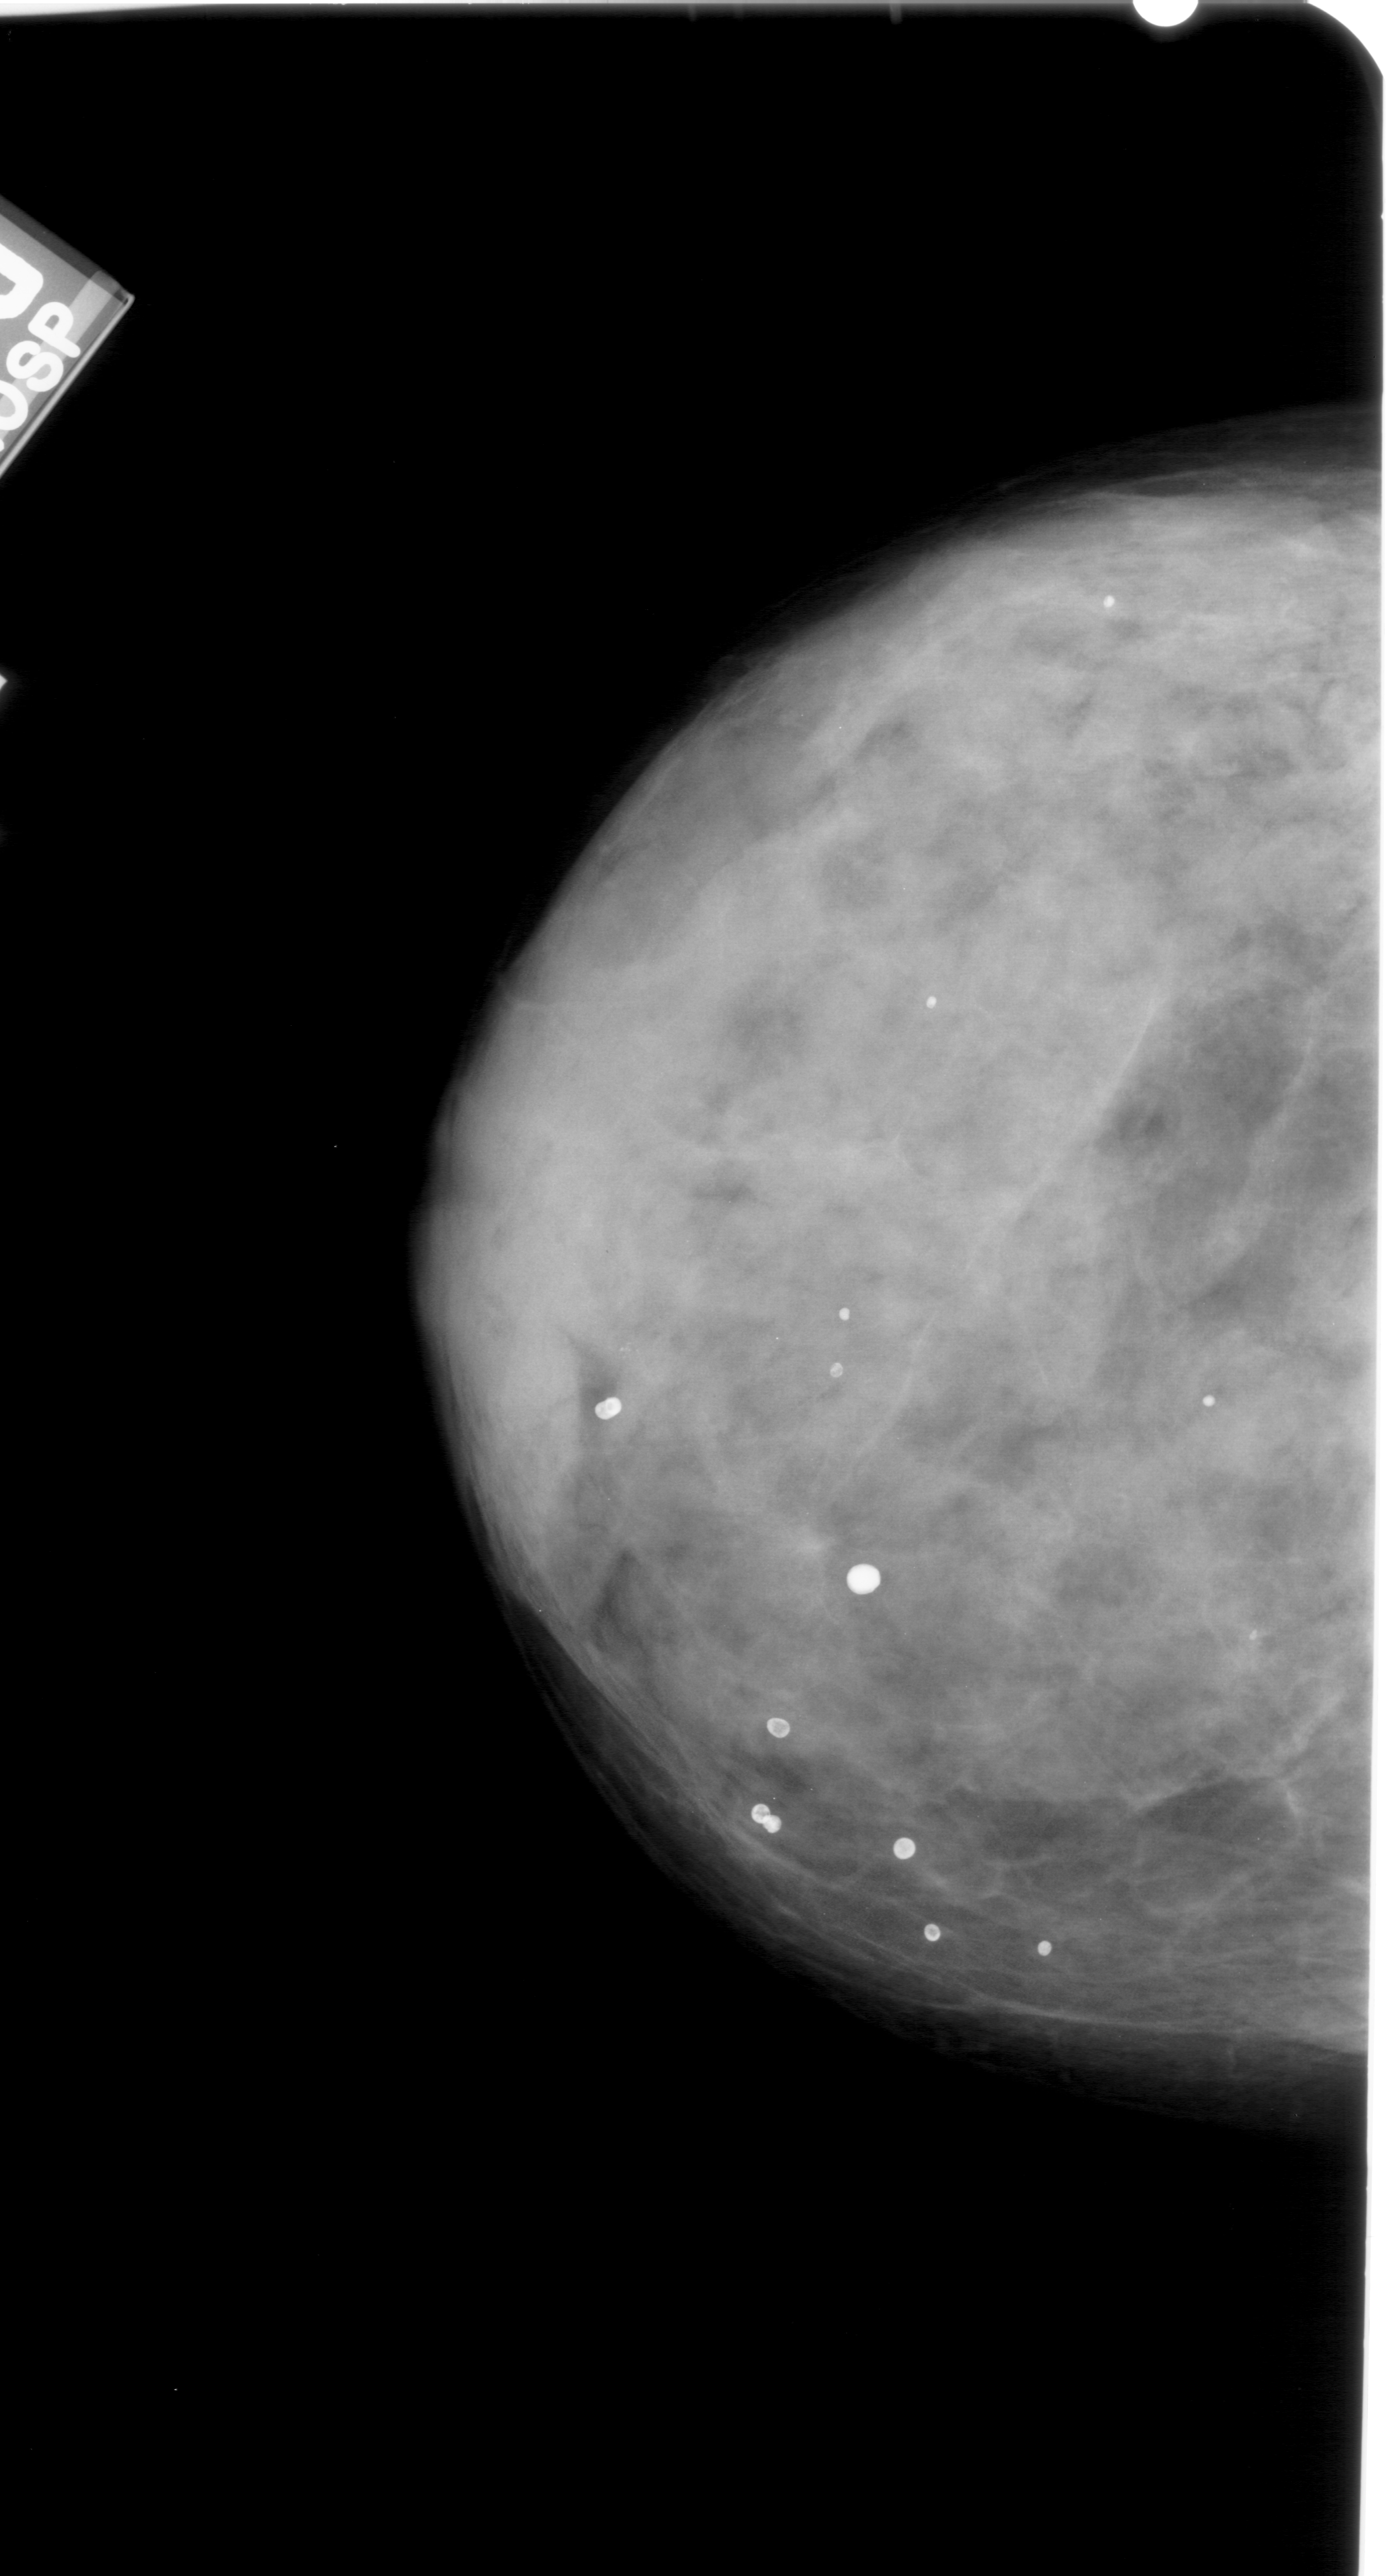
Scanned film-screen mammogram; left breast; craniocaudal (CC) view; breast composition: extremely dense (BI-RADS density category 4 of 4); 1389 × 2576 image matrix.
Expert-marked regions of interest on this image (one box per marked abnormality):
- calcifications, morphology amorphous, distribution clustered; BI-RADS assessment category 4; pathology (as recorded): benign: bounding box (x1, y1, x2, y2) in pixels: (543, 1280, 720, 1476)